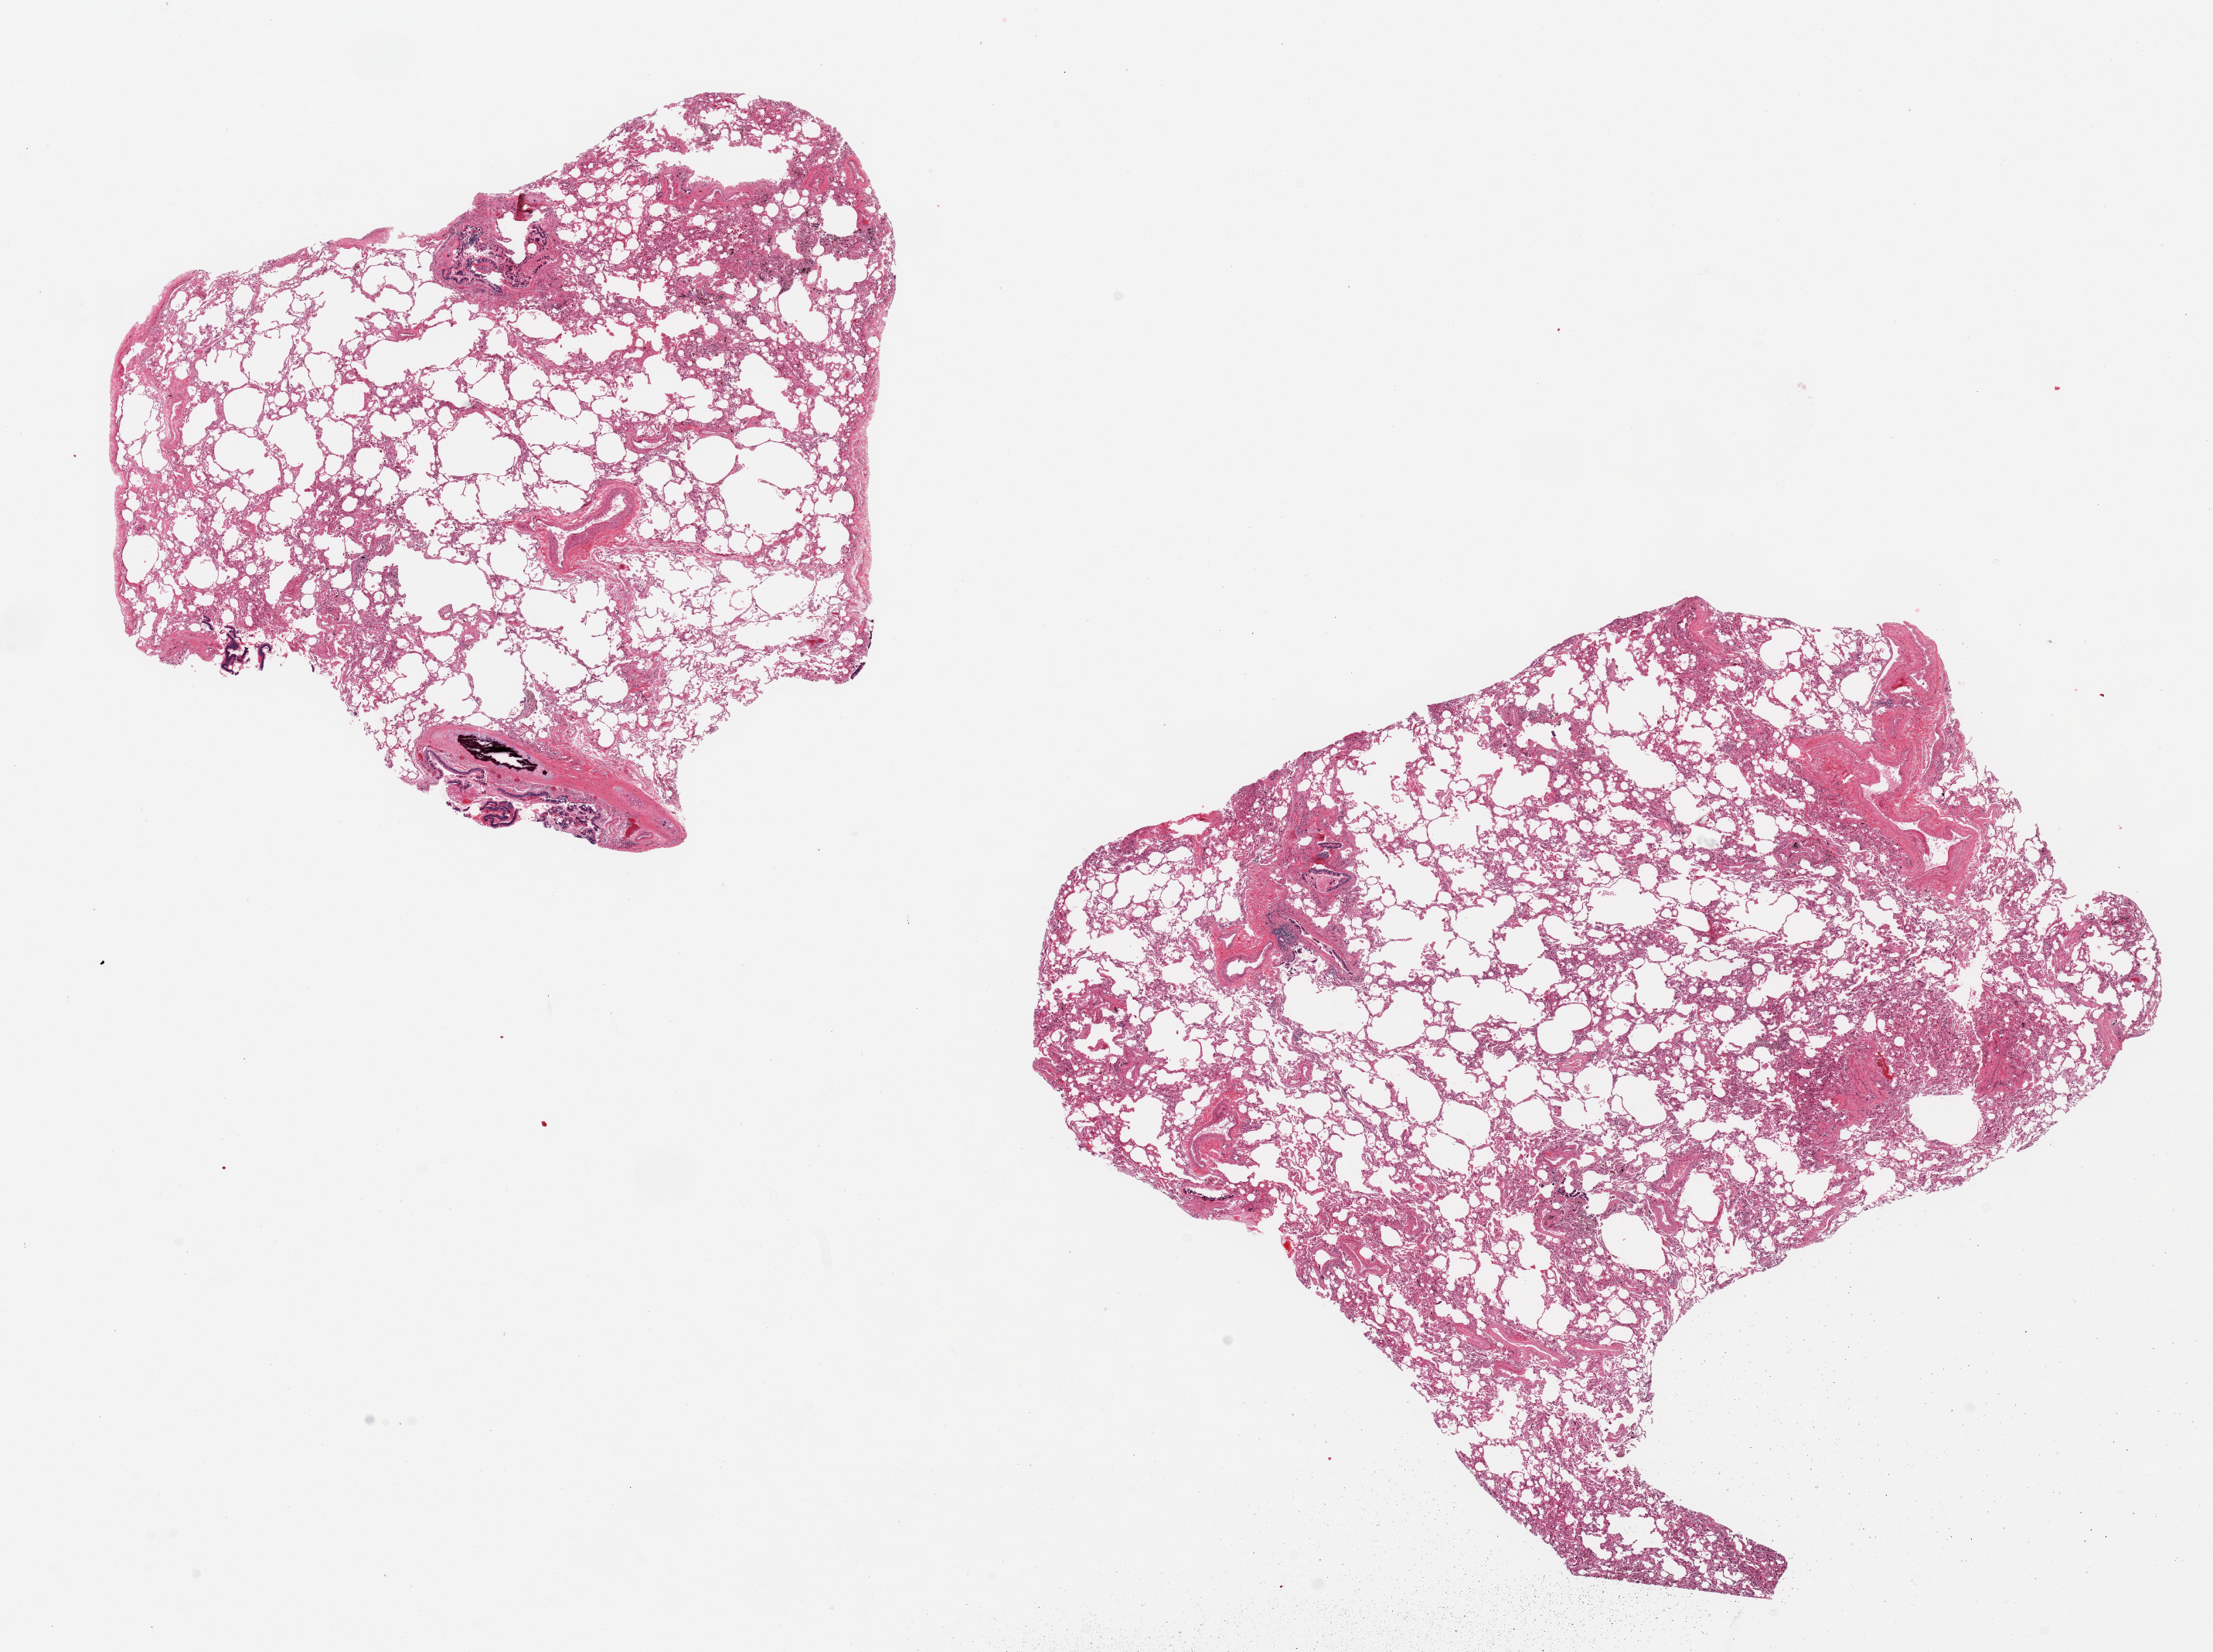
Digitized H&E-stained section — a low-resolution overview of the entire scanned area, about 22.6 x 16.9 mm (slide scanned at 20x), PAXgene-fixed paraffin-embedded (PFPE) section, target tissue: lung, tissue donor sample. Donor sex: male.
* review note (as recorded): 2 ~9x8mm aliquots, diffuse emphysematous changes, patchy chronic peribronchial inflammation